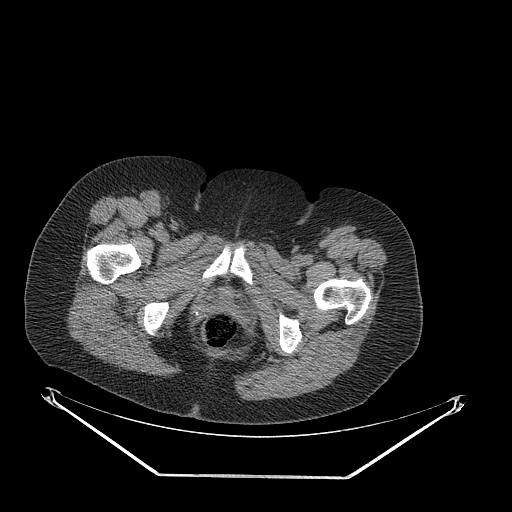
CT of an extremity soft-tissue mass (from a PET/CT study), one axial slice. Slice 61 of 257 in the series (ordered by position). Reconstruction kernel STANDARD. 140 kVp. Soft-tissue window (W 400 / L 40 HU). 512 × 512 image matrix. Female patient. From the clinical record (not read from this slice): histological type: synovial sarcoma; grade: intermediate; site of the primary tumour: right buttock.
Structures marked on this image (expert contour drawn on MRI and transferred to this co-registered scan by the dataset authors):
- gross tumour volume including surrounding oedema: bounding box <94,294,149,341> (left, top, right, bottom; pixels)